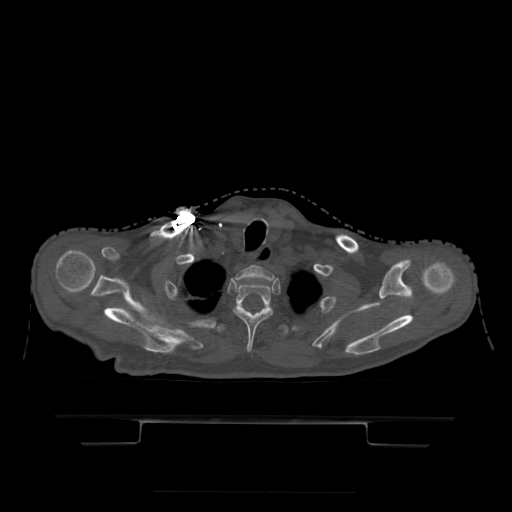
CT including the spine, one axial slice; position 385 of 522 along the scan axis; bone window (W 1800 / L 400 HU); 512 × 512 image matrix, field of view 436 × 436 mm. Patient age 68 years. From the clinical record (not read from this slice): primary cancer: urothelial.
Outlined on this slice (semi-automatically segmented with operator editing):
- T1 vertebra: bounding box (x1, y1, x2, y2) in pixels: (235, 266, 274, 281)
- T2 vertebra: (233, 282, 273, 353)
- T3 vertebra: (217, 307, 287, 336)